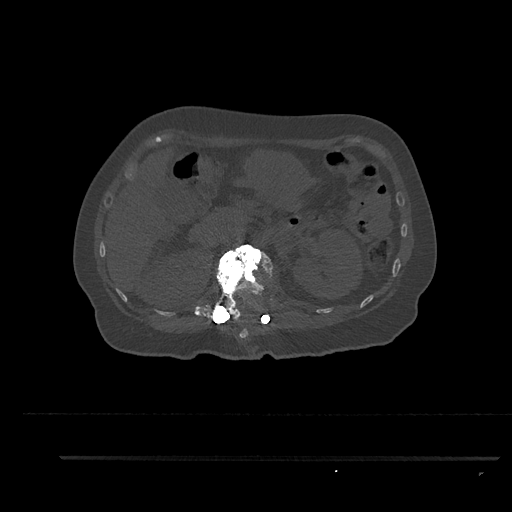
CT including the spine, one axial slice; position 226 of 797 along the scan axis; bone window (W 1800 / L 400 HU); 0.5 mm slice thickness; 512 × 512 image matrix, field of view 408 × 408 mm. Female patient, age 44 years. Case-level facts recorded for this patient, not image findings: primary cancer: renal; vertebrae with lytic lesions (as recorded): L1.
Outlined on this slice (semi-automatically segmented with operator editing):
- L1 vertebra: box from (x=205, y=243) to (x=274, y=324) px
- T12 vertebra: (x=229, y=310)–(x=249, y=338)